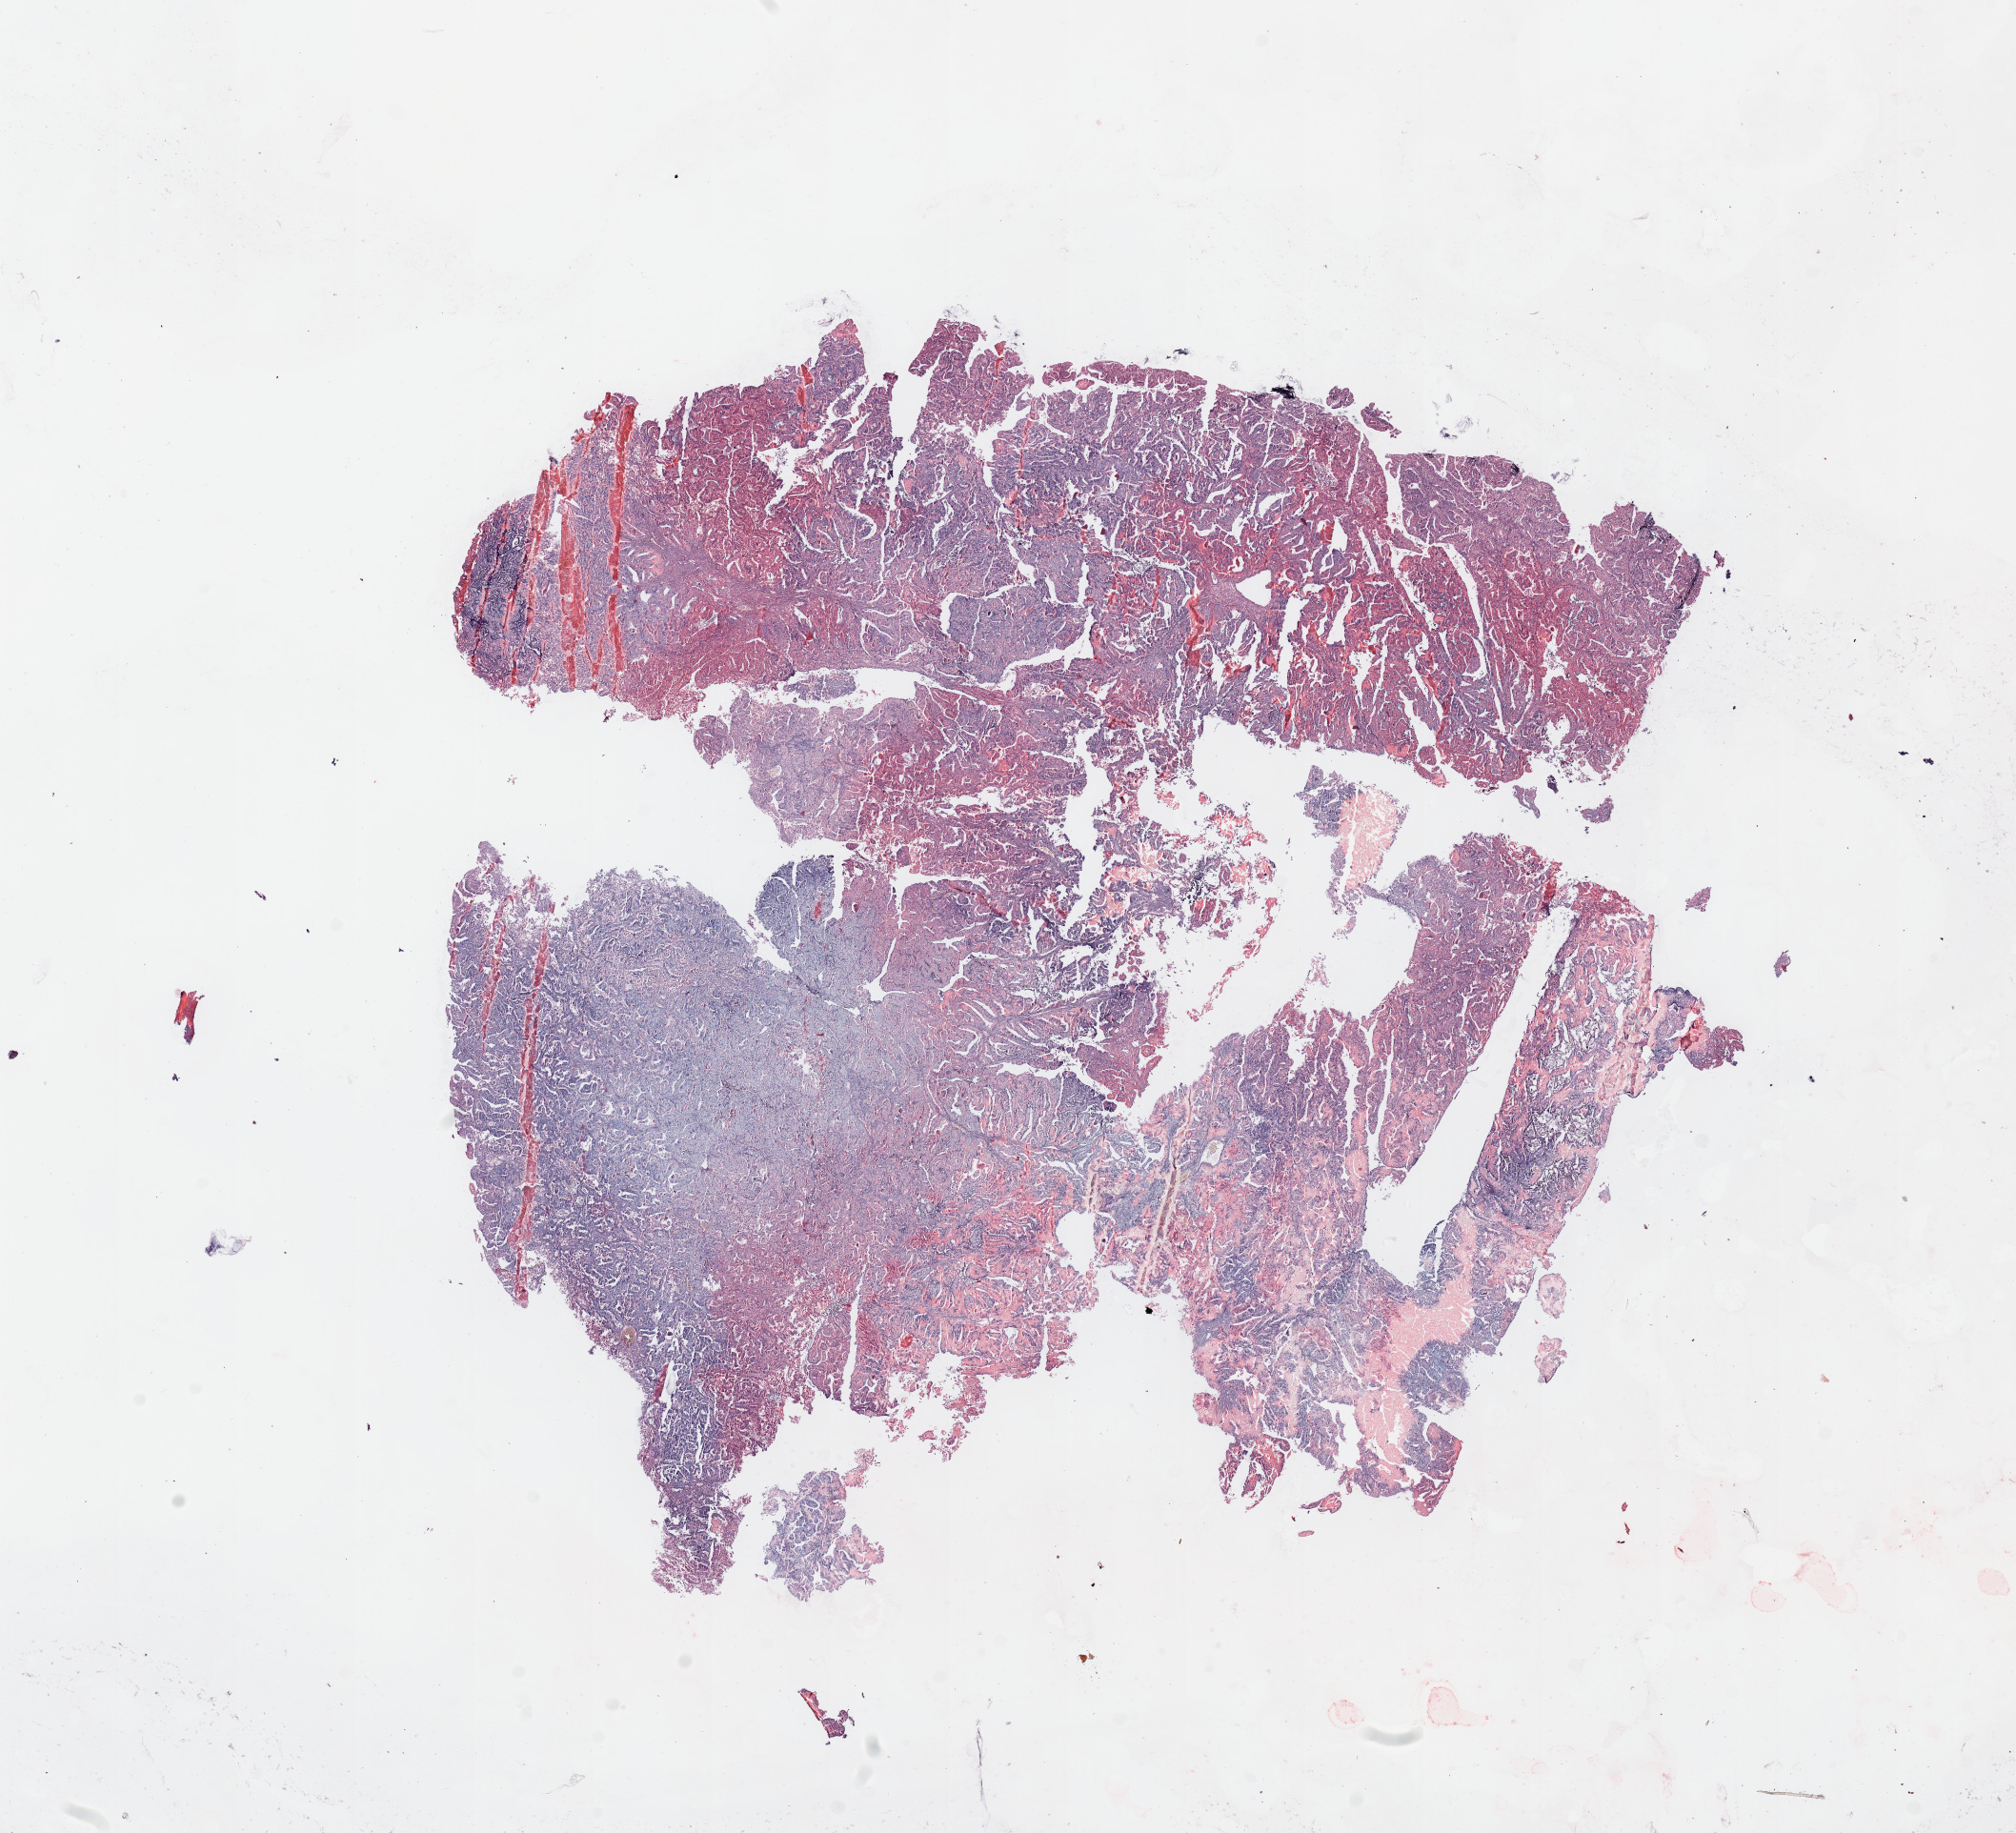
Whole-slide histology image, Hematoxylin and eosin (H&E) stained, whole scanned area (about 16.7 x 15.2 mm) shown as a low-resolution overview; tumour tissue sample, sampled site: uterus. Patient: female, age 70 years. Histologic grade: G2 (moderately differentiated). Composition of this section per pathologist review: tumour nuclei 98%, necrosis 2%.
AJCC pathologic stage: I. Diagnosis: Endometrioid adenocarcinoma, NOS.